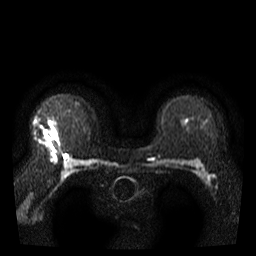
Breast MRI, one axial slice; position 26 of 40 along the scan axis; diffusion-weighted series; image 2 of 4 stored at this slice position (different b-values; order by instance number); 3 T; 5 mm slice thickness; 256 × 256 image matrix, field of view 300 × 300 mm. Female patient.
Structures marked on this image (outlined manually by an expert reader):
- tumour on diffusion-weighted imaging: box from (x=47, y=129) to (x=55, y=138) px